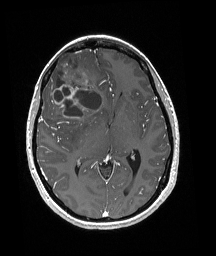
Brain MRI from a brain-tumour surgery series, one axial slice; position 101 of 192 along the scan axis; T1-weighted post-contrast; 216 × 256 image matrix. From the clinical record (not read from this slice): histopathology: Oligodendroglioma; WHO grade: 3; IDH mutation: yes; tumour location: Right Frontal.
Structures marked on this image (expert manual segmentation):
- tumour: bounding box (x1, y1, x2, y2) in pixels: (48, 53, 102, 118)